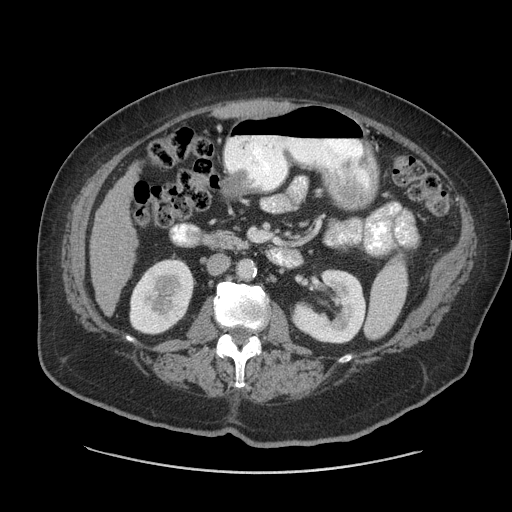
Contrast-enhanced abdominal CT (liver protocol), one axial slice. Reconstruction kernel STANDARD. Soft-tissue window (W 400 / L 40 HU). 2.5 mm slice thickness. 512 × 512 image matrix. Case-level facts recorded for this patient, not image findings: diagnosis: hepatocellular carcinoma (patient treated with transarterial chemoembolisation; whether this scan precedes or follows treatment is not stated here); TNM stage (as recorded): Stage-I; Child-Pugh class: A; tumour differentiation: well differentiated.
Structures marked on this image (semi-automatic segmentation, software-assisted and operator-edited):
- liver parenchyma outside the tumour (the mass and vessels are separate outlines, so this box may not span the whole liver): bounding box [x1, y1, x2, y2] px = [90, 166, 138, 314]